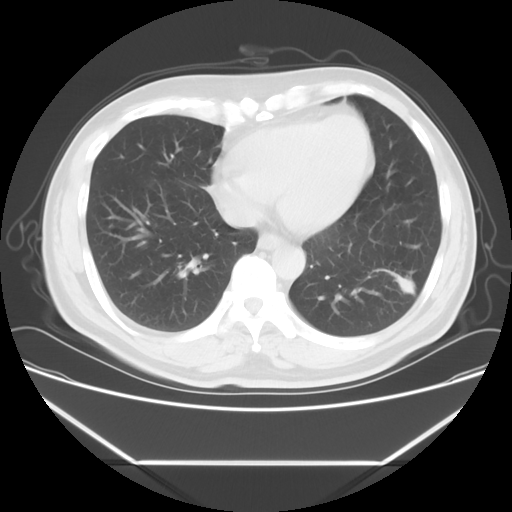
Chest CT, one axial slice; slice 20 of 57 in the series (ordered by position); 120 kVp; lung window (W 1500 / L -600 HU); 5 mm slice thickness; 512 × 512 image matrix, field of view 384 × 384 mm. Patient: male, 53 years. From the clinical record (not read from this slice): clinical TNM (as recorded): T1c N0 M0.
Outlined on this slice (bounding box drawn by a radiologist):
- lung tumour (recorded histology: adenocarcinoma): bounding box <375,264,419,303> (left, top, right, bottom; pixels)